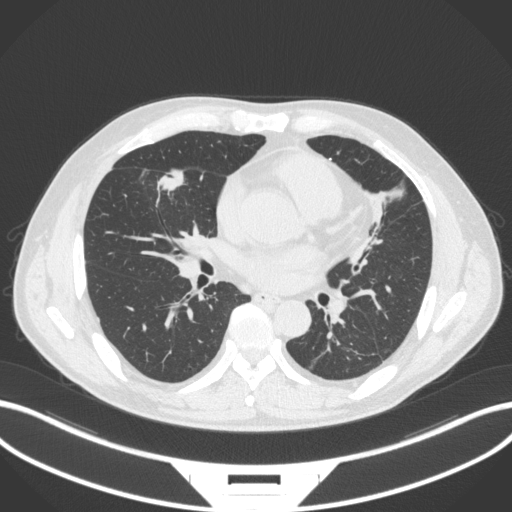
Chest CT, one axial slice; slice 149 of 399 in the series (ordered by position); reconstruction kernel B31f; lung window (W 1500 / L -600 HU); 1 mm slice thickness; 512 × 512 image matrix. Patient: male, 59 years. From the clinical record (not read from this slice): clinical TNM (as recorded): T2a N1 M0.
Annotated regions visible in this slice (bounding box drawn by a radiologist):
- lung tumour (recorded histology: adenocarcinoma): bounding box (x1, y1, x2, y2) in pixels: (156, 162, 189, 193)